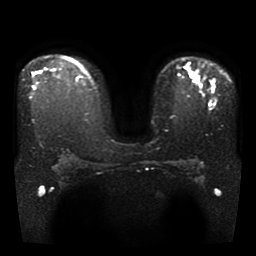
Breast MRI, one axial slice; position 25 of 37 along the scan axis; diffusion-weighted series; image 2 of 4 stored at this slice position (different b-values; order by instance number); 1.5 T; 5 mm slice thickness; 256 × 256 image matrix, field of view 330 × 330 mm. Female patient.
Annotated regions visible in this slice (manually delineated by an expert):
- tumour on diffusion-weighted imaging: bounding box <187,67,197,77> (left, top, right, bottom; pixels)